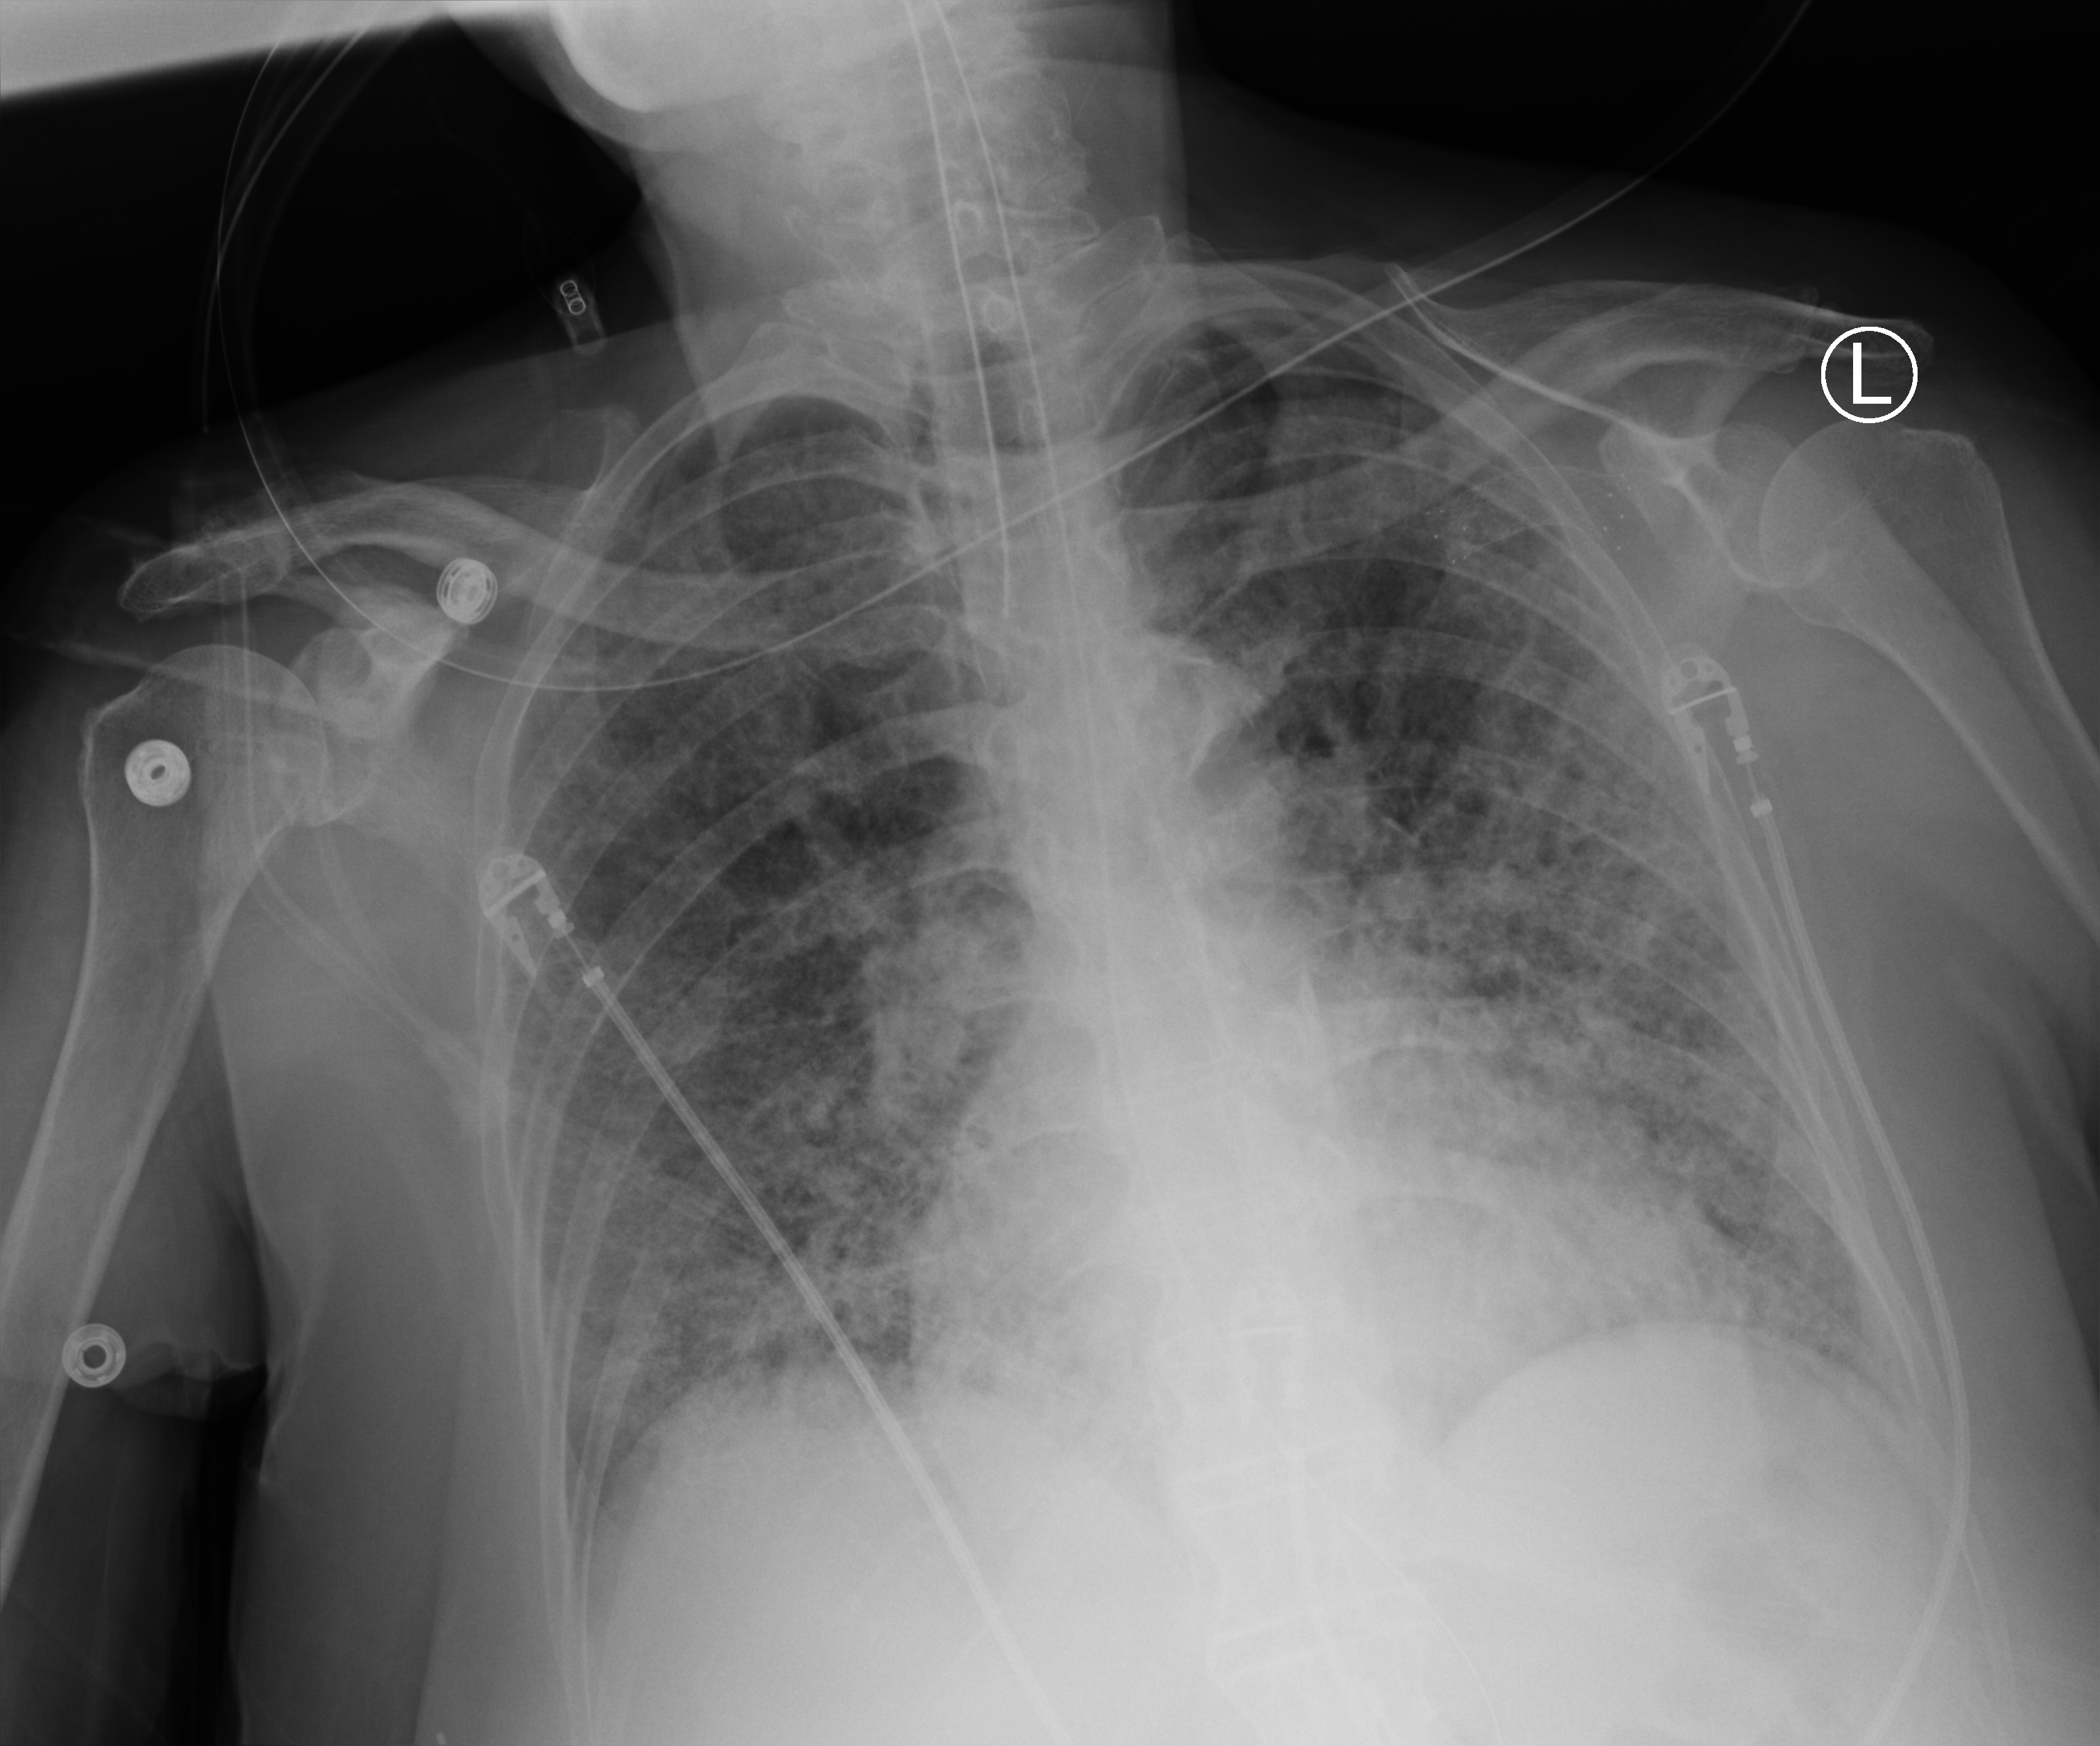
Bedside chest radiograph (computed radiography), anteroposterior (AP) projection. Patient hospitalised with COVID-19; female, aged 60–74 years.
Admission-level facts for this patient (not findings on this image; timing relative to this image not recorded): admitted to intensive care during this hospital stay: yes; mechanically ventilated during this hospital stay: yes; other chronic lung disease (admission record): no.